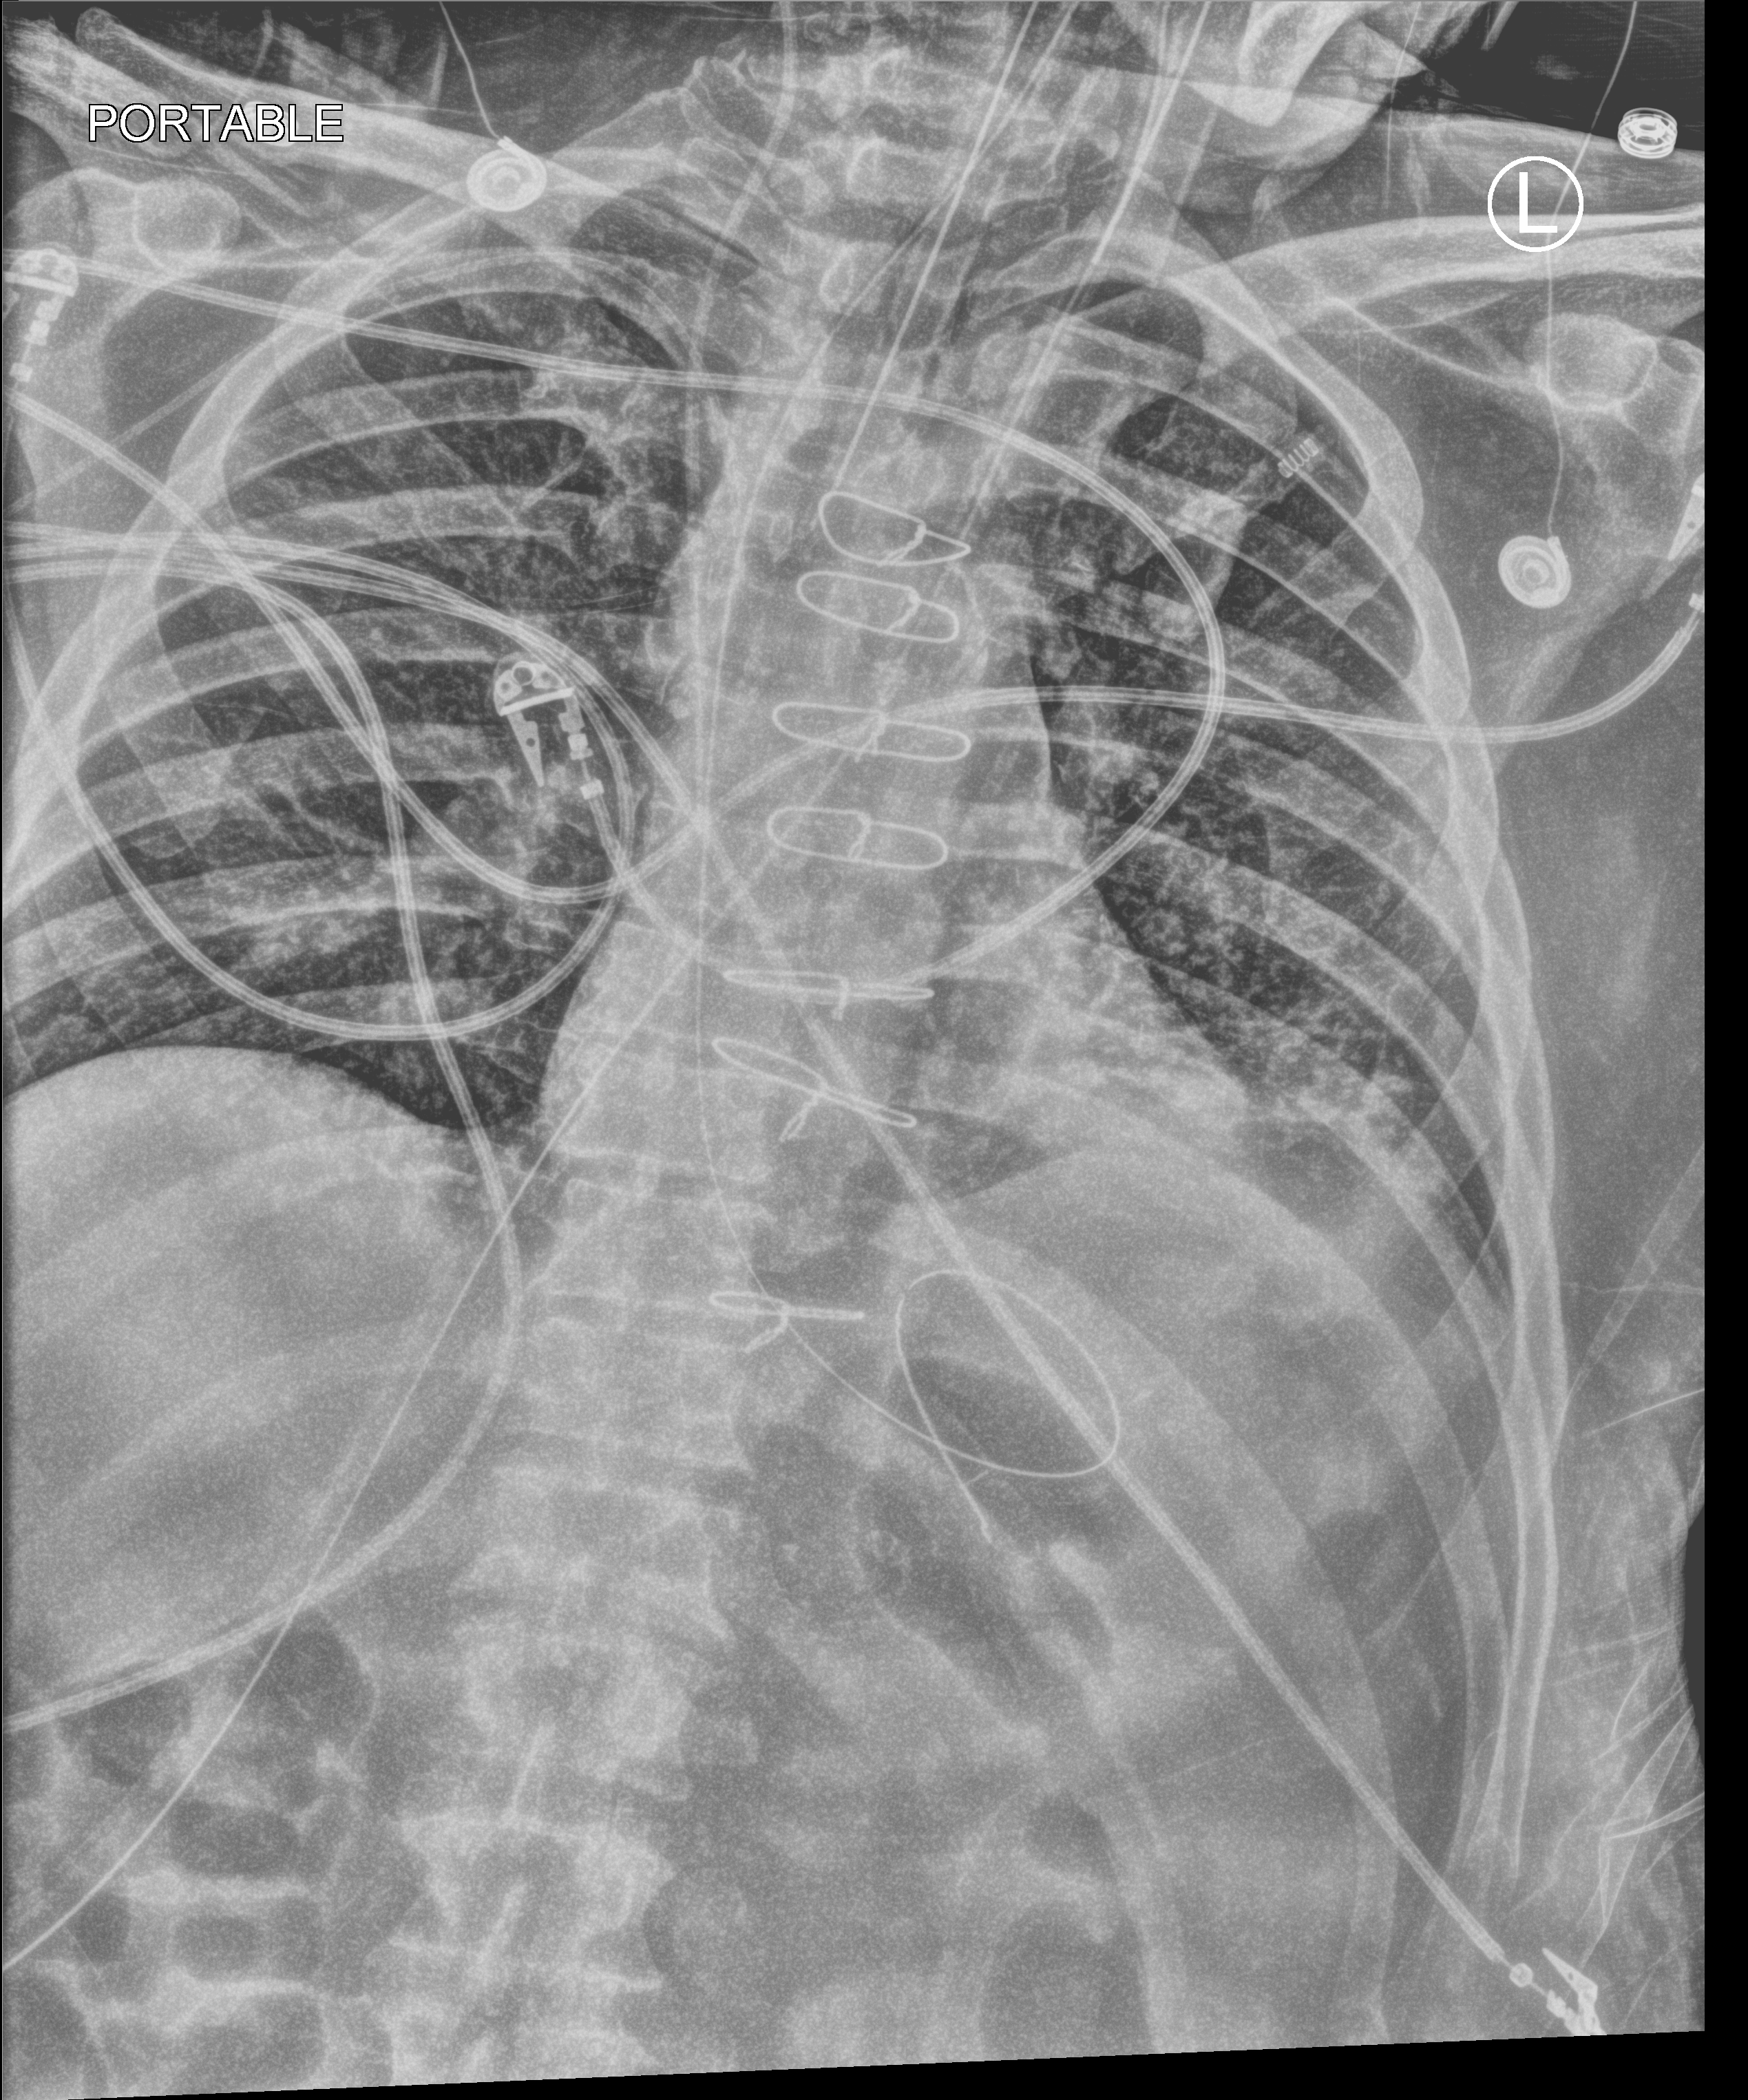
Chest X-ray (portable), anteroposterior (AP) projection. Male patient hospitalised with COVID-19, age 60–74 years.
Admission-level facts for this patient (not findings on this image; timing relative to this image not recorded): admitted to intensive care during this hospital stay: yes; mechanically ventilated during this hospital stay: yes.